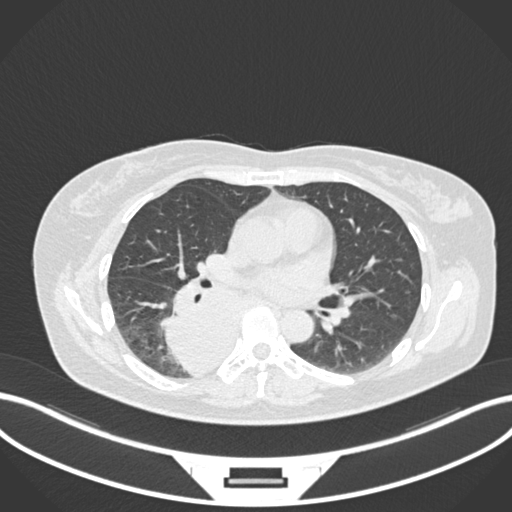
Chest CT, one axial slice; position 591 of 677 along the scan axis; lung window (W 1500 / L -600 HU); 512 × 512 image matrix, field of view 400 × 400 mm. Patient: female, 54 years. Case-level facts recorded for this patient, not image findings: clinical TNM (as recorded): T4 N0 M0.
Annotated regions visible in this slice (rectangle marked by the reading radiologist):
- lung tumour (recorded histology: adenocarcinoma): box from (x=150, y=272) to (x=247, y=378) px